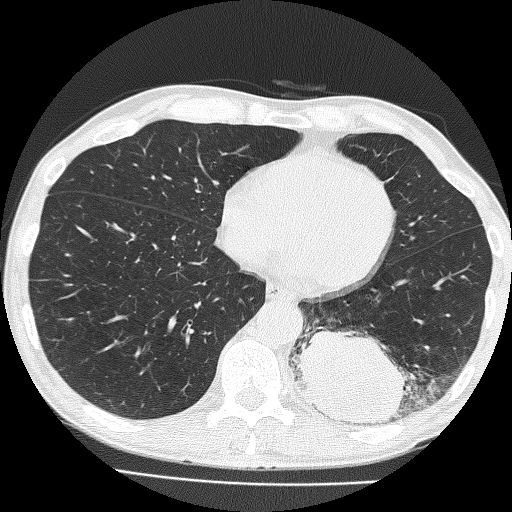
Low-dose screening chest CT, axial slice. First (baseline) screen. Lung window (W 1500 / L -600 HU). 512 × 512 image matrix, field of view 324 × 324 mm. Male, age 58 years at enrolment. Current smoker at enrolment.
Expert-annotated lung lesion, bounding box <293,299,427,435> (left, top, right, bottom; pixels). The screening reader recorded 2 non-calcified nodules or masses ≥4 mm on this exam; which of them this box marks is not recorded. Lung cancer was diagnosed 39 days after this screen: non-small cell carcinoma, left lower lobe, poorly differentiated (G3), stage IV (AJCC 6th edition), 74 mm at pathology.